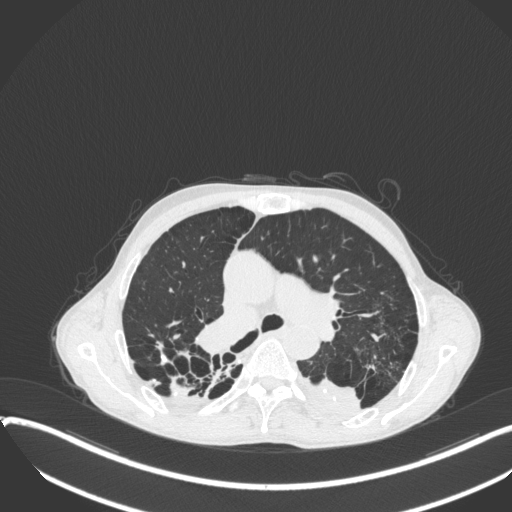
Chest CT, one axial slice; slice 247 of 400 in the series (ordered by position); reconstruction kernel B31f; 120 kVp; lung window (W 1500 / L -600 HU); 1 mm slice thickness; 512 × 512 image matrix, field of view 400 × 400 mm. Patient: male, 57 years. From the clinical record (not read from this slice): clinical TNM (as recorded): T4 N0 M0.
Structures marked on this image (rectangle marked by the reading radiologist):
- lung tumour (recorded histology: squamous cell carcinoma): bounding box (x1, y1, x2, y2) in pixels: (296, 371, 364, 418)